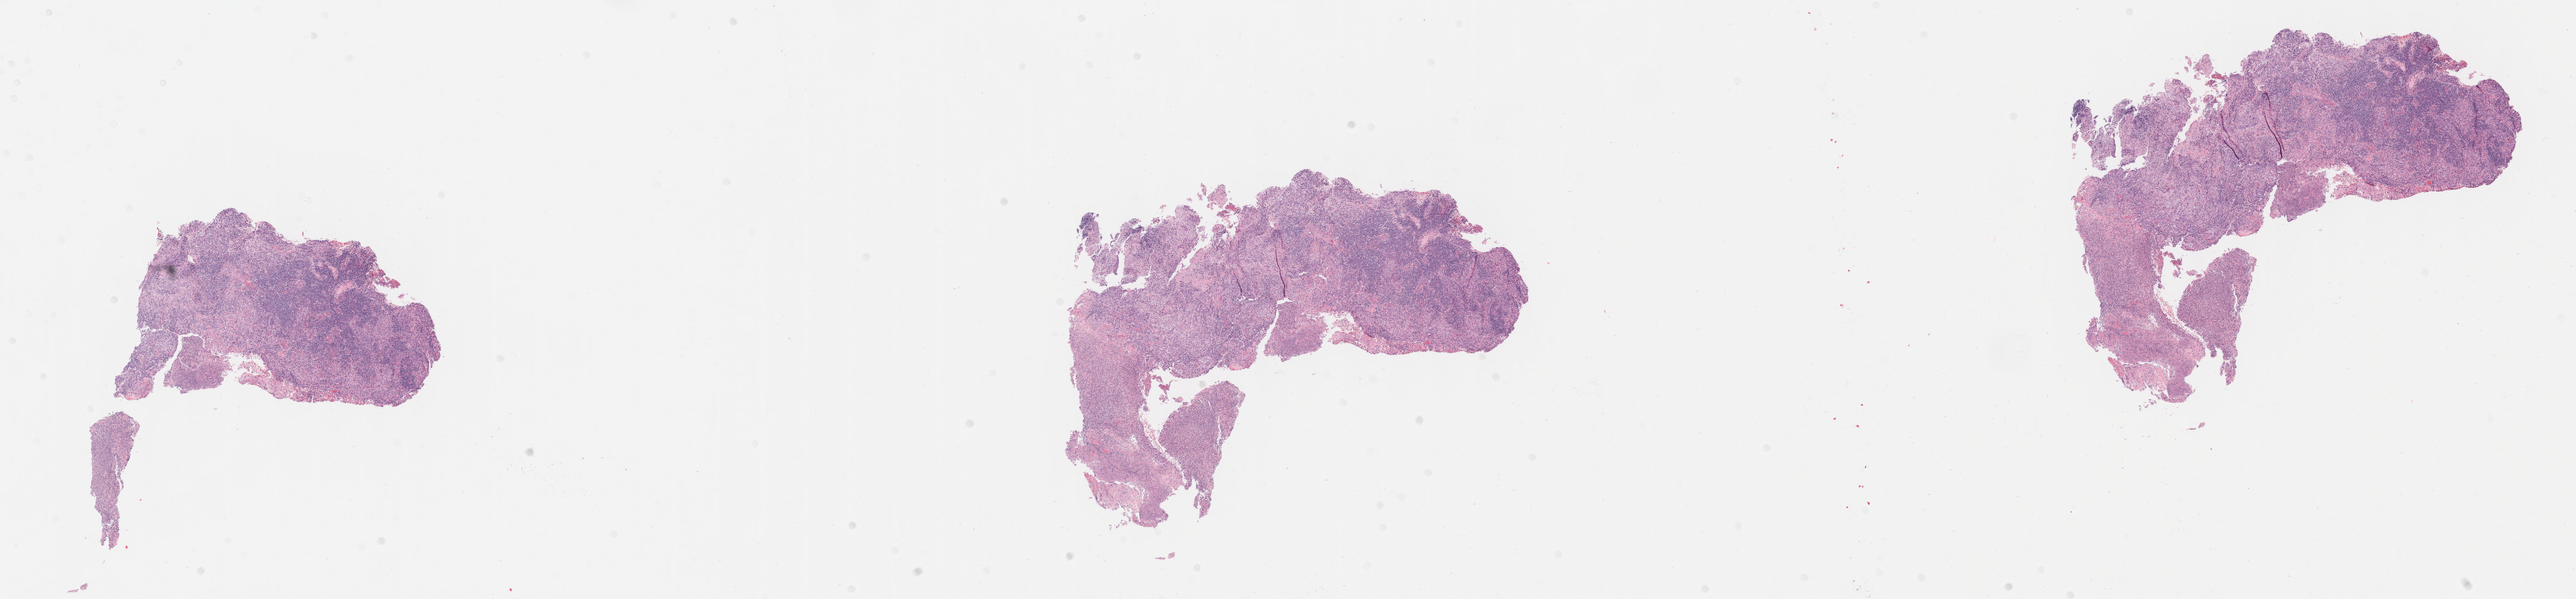
Whole-slide image, haematoxylin and eosin stain, shown as a low-resolution overview of the whole scanned area (about 29.2 x 6.8 mm); specimen: tumor tissue; anatomic site: cervix. Patient: female, age 39 years.
Histologic diagnosis: Squamous cell carcinoma, large cell, nonkeratinizing, NOS.